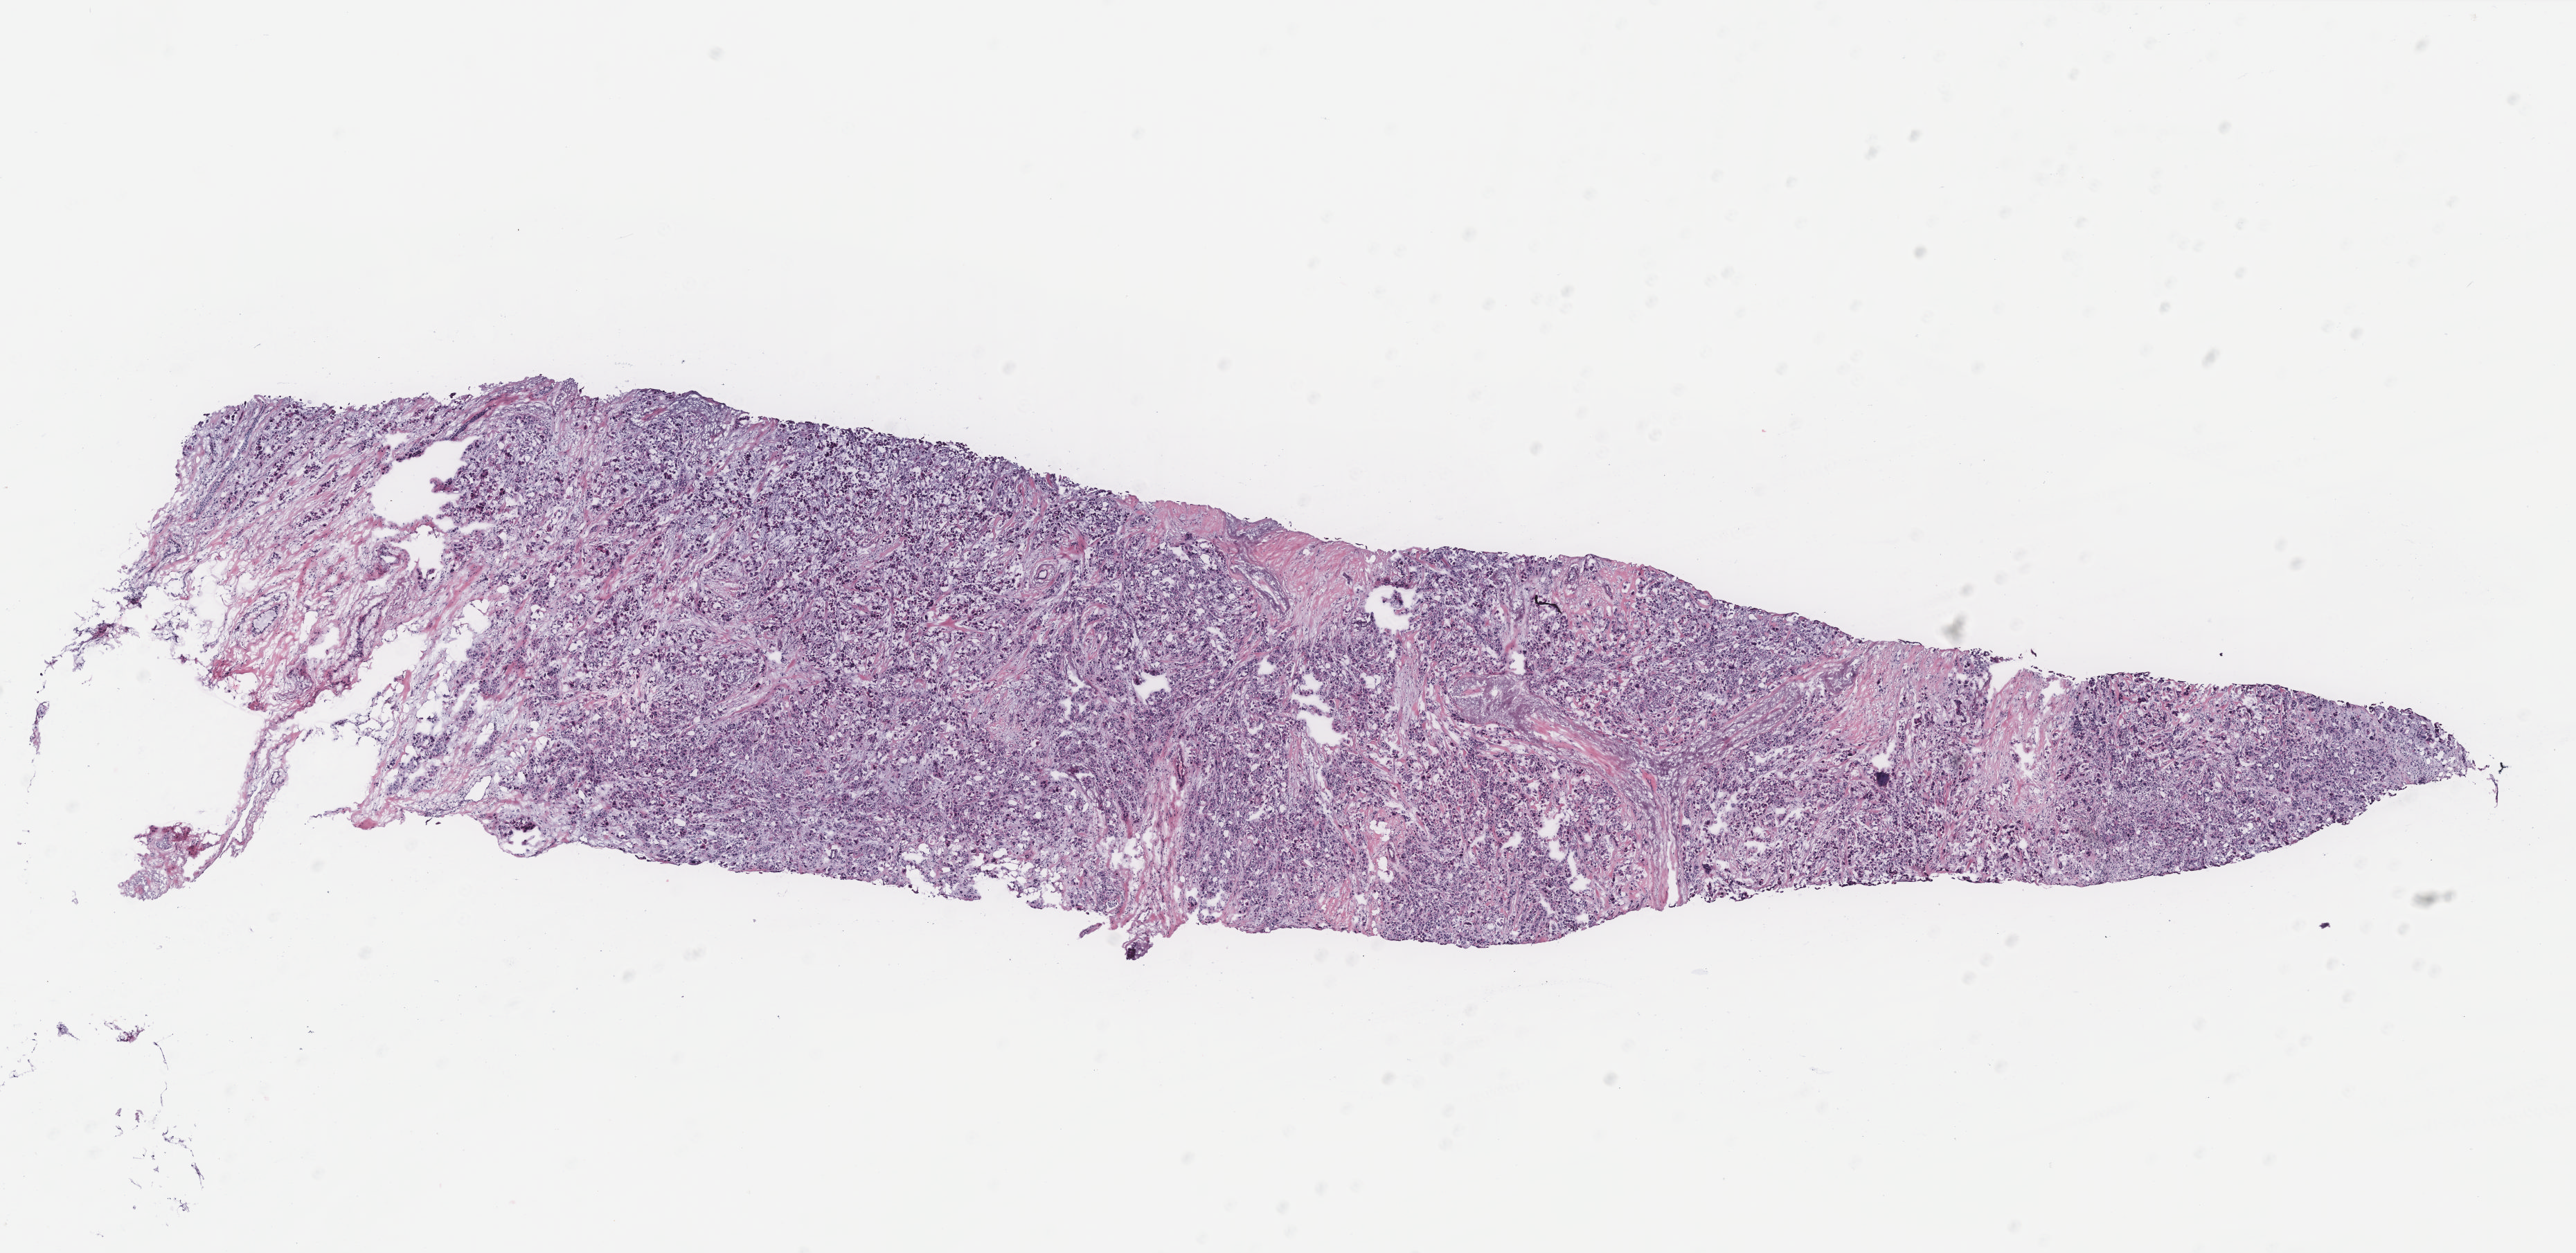
H&E-stained whole-slide image, a low-resolution overview of the entire scanned area, about 14.9 x 7.2 mm (from a 40x scan); tumour tissue sample, breast. Female, 88 y/o.
Diagnosis: Infiltrating duct carcinoma, NOS.